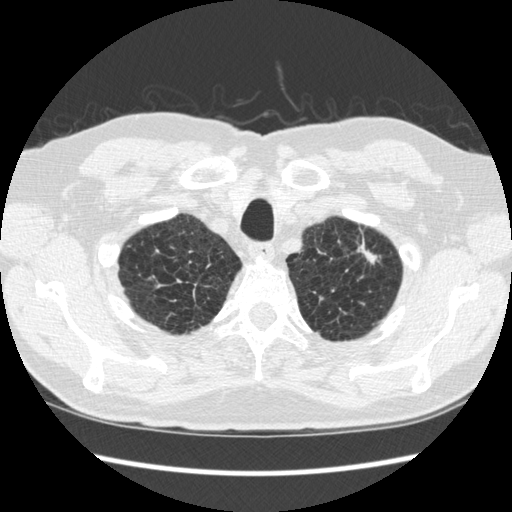
Chest CT (low-dose screening protocol), one axial image, second screening round (one year after baseline), lung window (W 1500 / L -600 HU), 1.25 mm slice thickness. Male participant, aged 70 years at enrolment.
- Expert reader's lesion annotation, box from (x=327, y=228) to (x=389, y=296) px.
- The screening reader recorded 5 non-calcified nodules or masses ≥4 mm on this exam (right lower lobe, right lower lobe, right lower lobe, left upper lobe, left lower lobe); which of them this box marks is not recorded.
- Lung cancer was diagnosed 479 days after this screen: squamous cell carcinoma, NOS, left upper lobe, moderately differentiated (G2), stage IA (AJCC 6th edition), 18 mm at pathology.